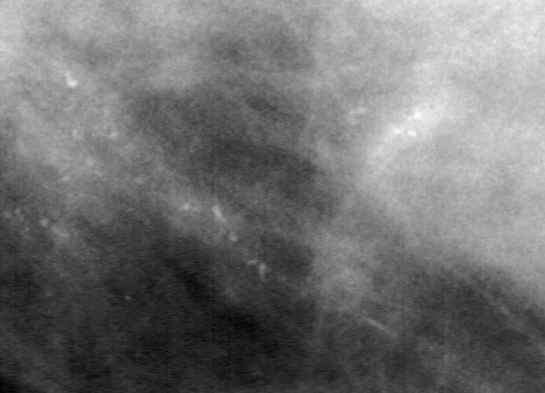
Cropped region of a digitized screen-film mammogram centred on a radiologist-marked abnormality; left breast; CC view; BI-RADS breast density category 4 (scale 1–4).
Marked abnormality: calcifications, morphology pleomorphic, distribution linear; BI-RADS assessment category 4; pathology result (as recorded, not read from the image): malignant.